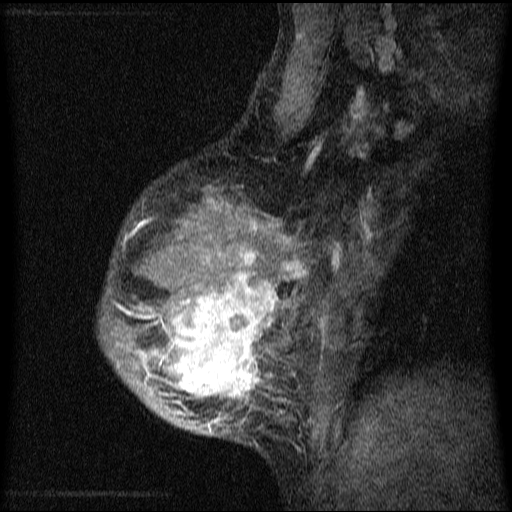
Breast MRI (dynamic contrast-enhanced), one sagittal slice; position 49 of 64 along the scan axis; dynamic contrast-enhanced series, image 2 of 4 at this slice position (ordered by acquisition); 1.5 T; TE 4.2 ms, TR 9.1 ms; 2 mm slice thickness; 512 × 512 image matrix, field of view 180 × 180 mm. Female patient, age 33 years.
Outlined on this slice (semi-automatic segmentation, software-assisted and operator-edited):
- analysis volume of interest (the breast-tissue region the enhancement analysis was run in; not a lesion): bounding box <100,153,336,457> (left, top, right, bottom; pixels)
- tumour enhancement mask (voxels above the 70 % enhancement threshold inside the analysis volume of interest): <114,199,304,433>